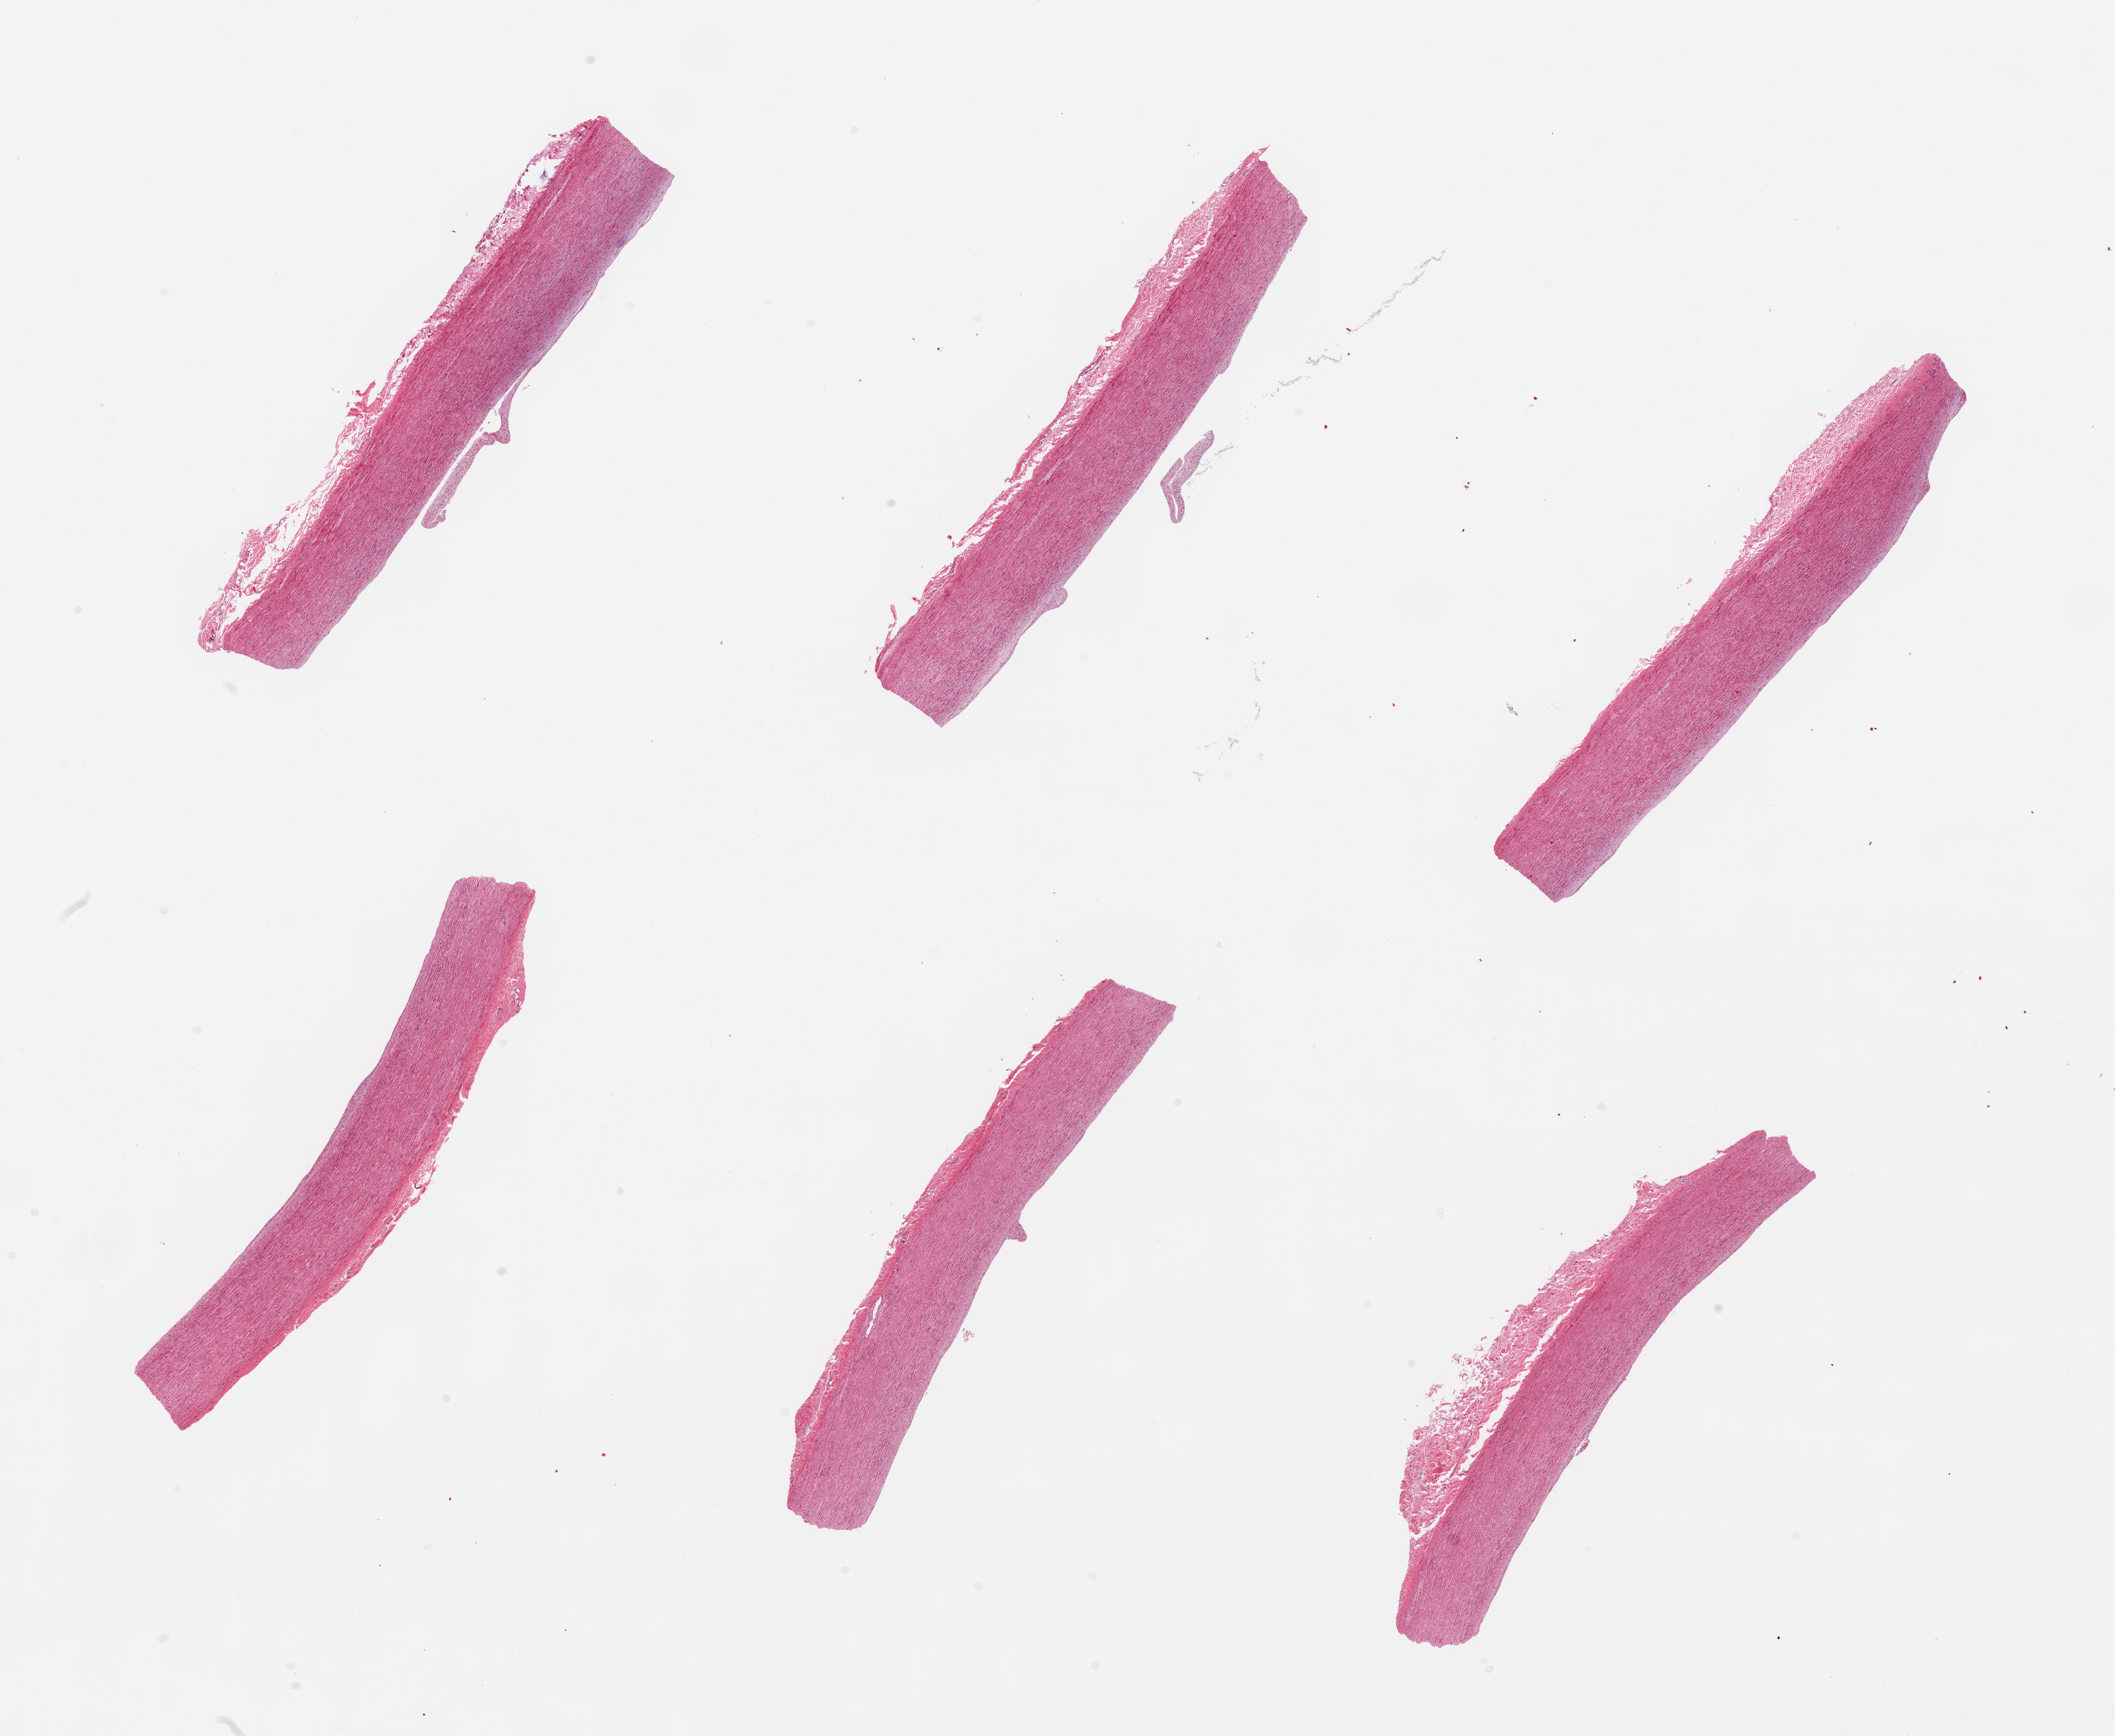
Hematoxylin and eosin (H&E) whole-slide image — shown as a low-resolution overview of the whole scanned area (about 23.6 x 19.4 mm). PAXgene-fixed paraffin-embedded (PFPE) section. Section of aorta (target tissue). Donor tissue sample. Male donor.
Pathologist's review note for this sample: 6 pieces; suggestive of evolving atherosis; 0.4mm attached adventitia.